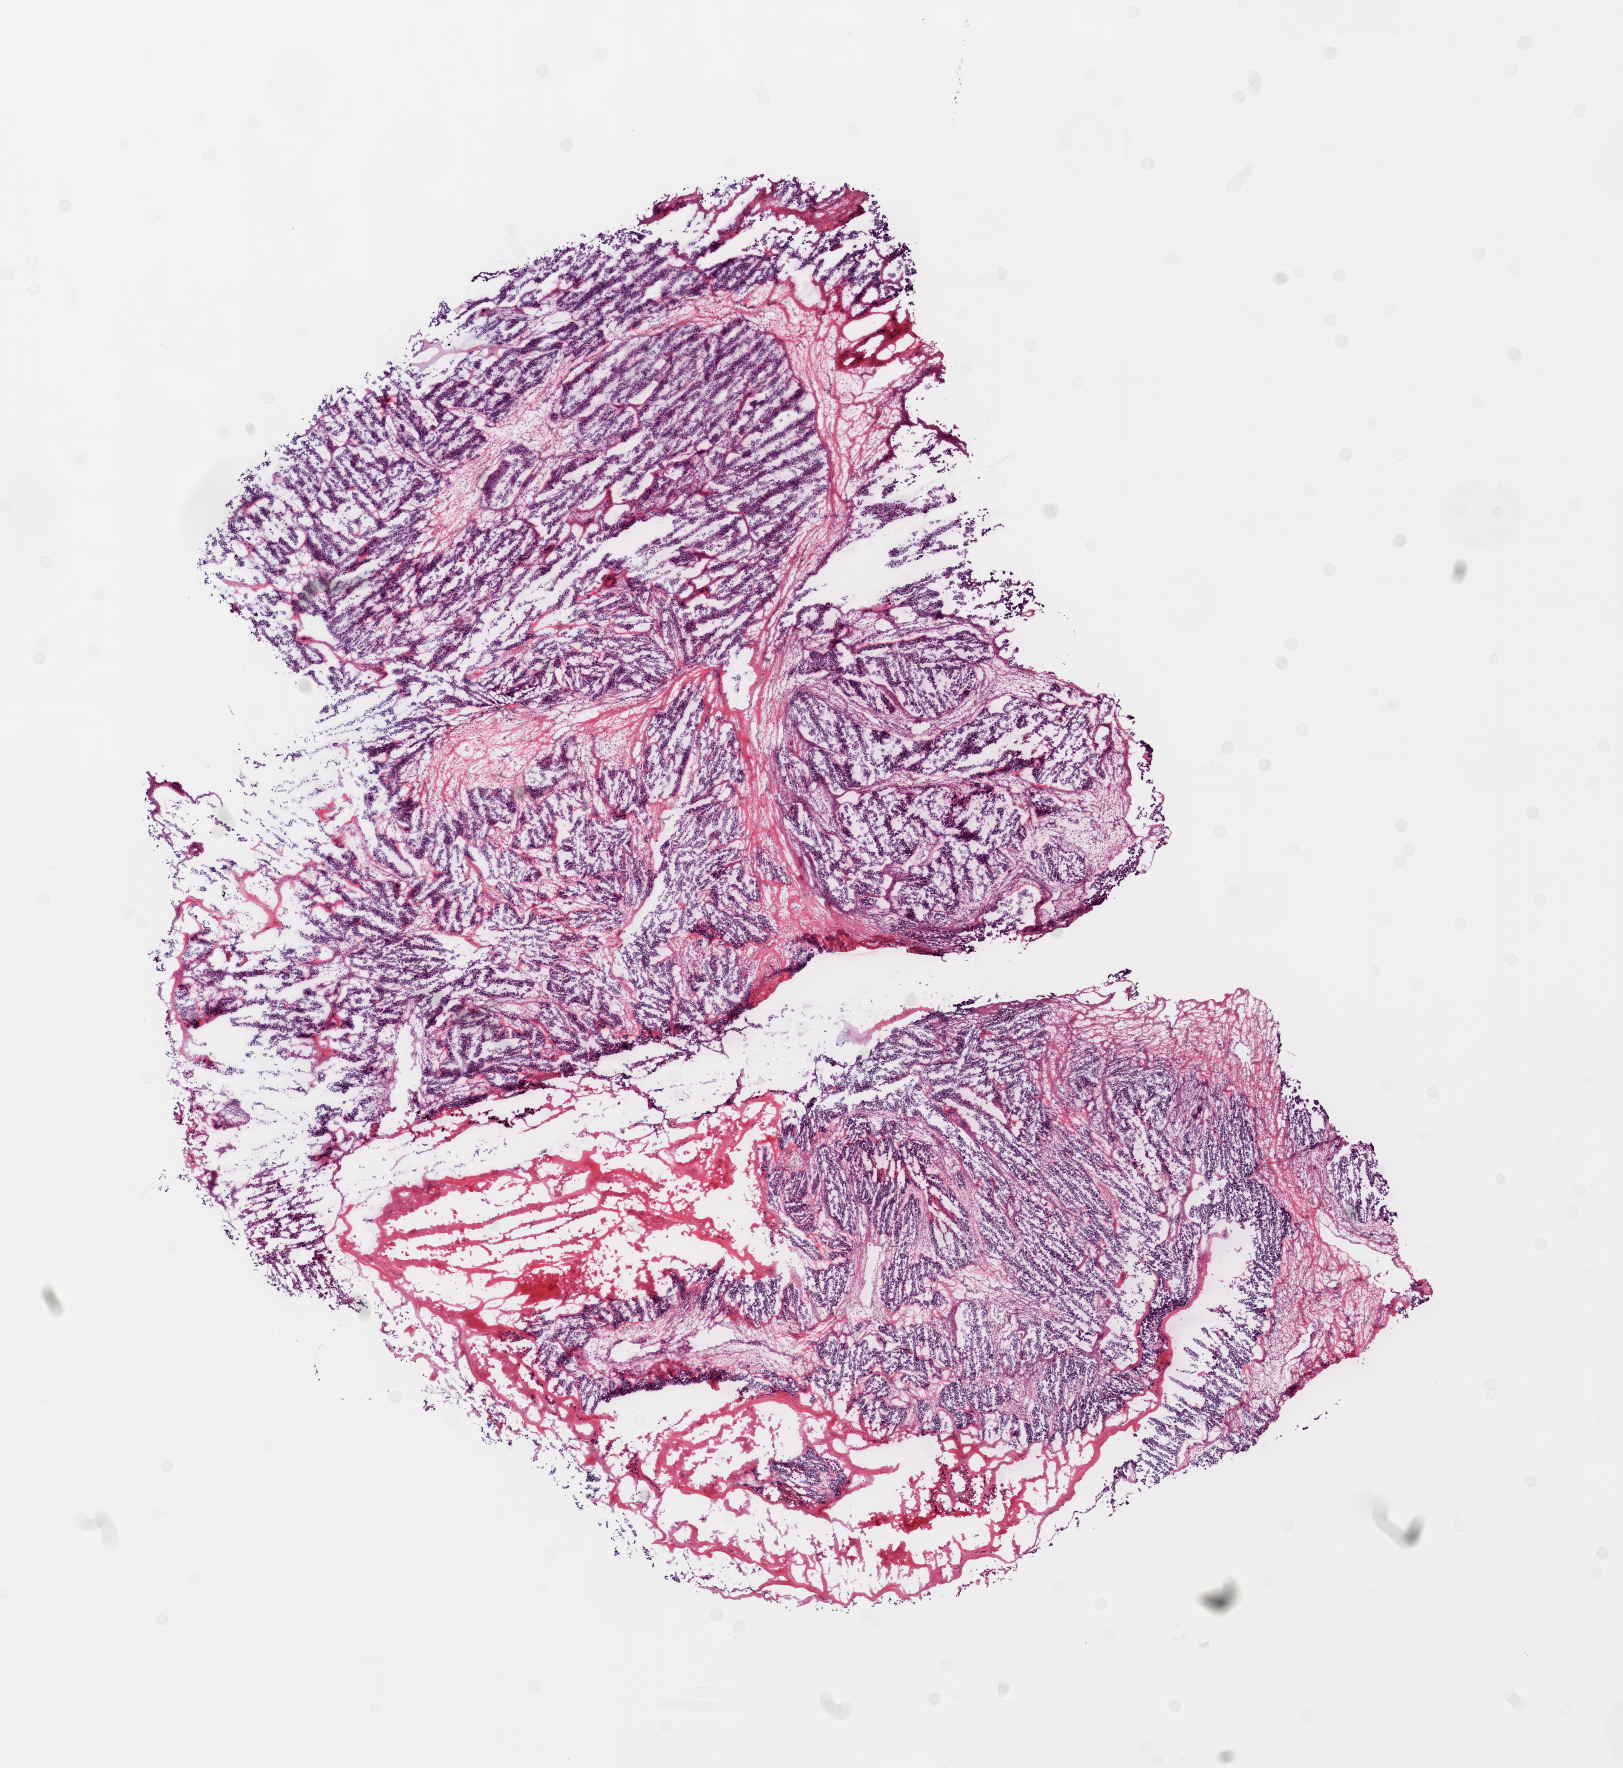
Digitized Hematoxylin and eosin (H&E) stained tissue section (whole slide) — a low-resolution overview of the entire scanned area, about 13.0 x 14.1 mm (slide scanned at 20x). Frozen section from the top of the tissue portion. Primary tumour sample from the ovary. Patient: female, age at initial diagnosis 78 years. Histologic grade: G3 (poorly differentiated). Pathologist review of this section (percent, as recorded): tumour cells 65%, tumour nuclei 85%, normal cells 15%, stromal cells 0%, necrosis 20%.
FIGO stage: IIIC. Pathologic diagnosis: Serous cystadenocarcinoma, NOS. Laterality: right.